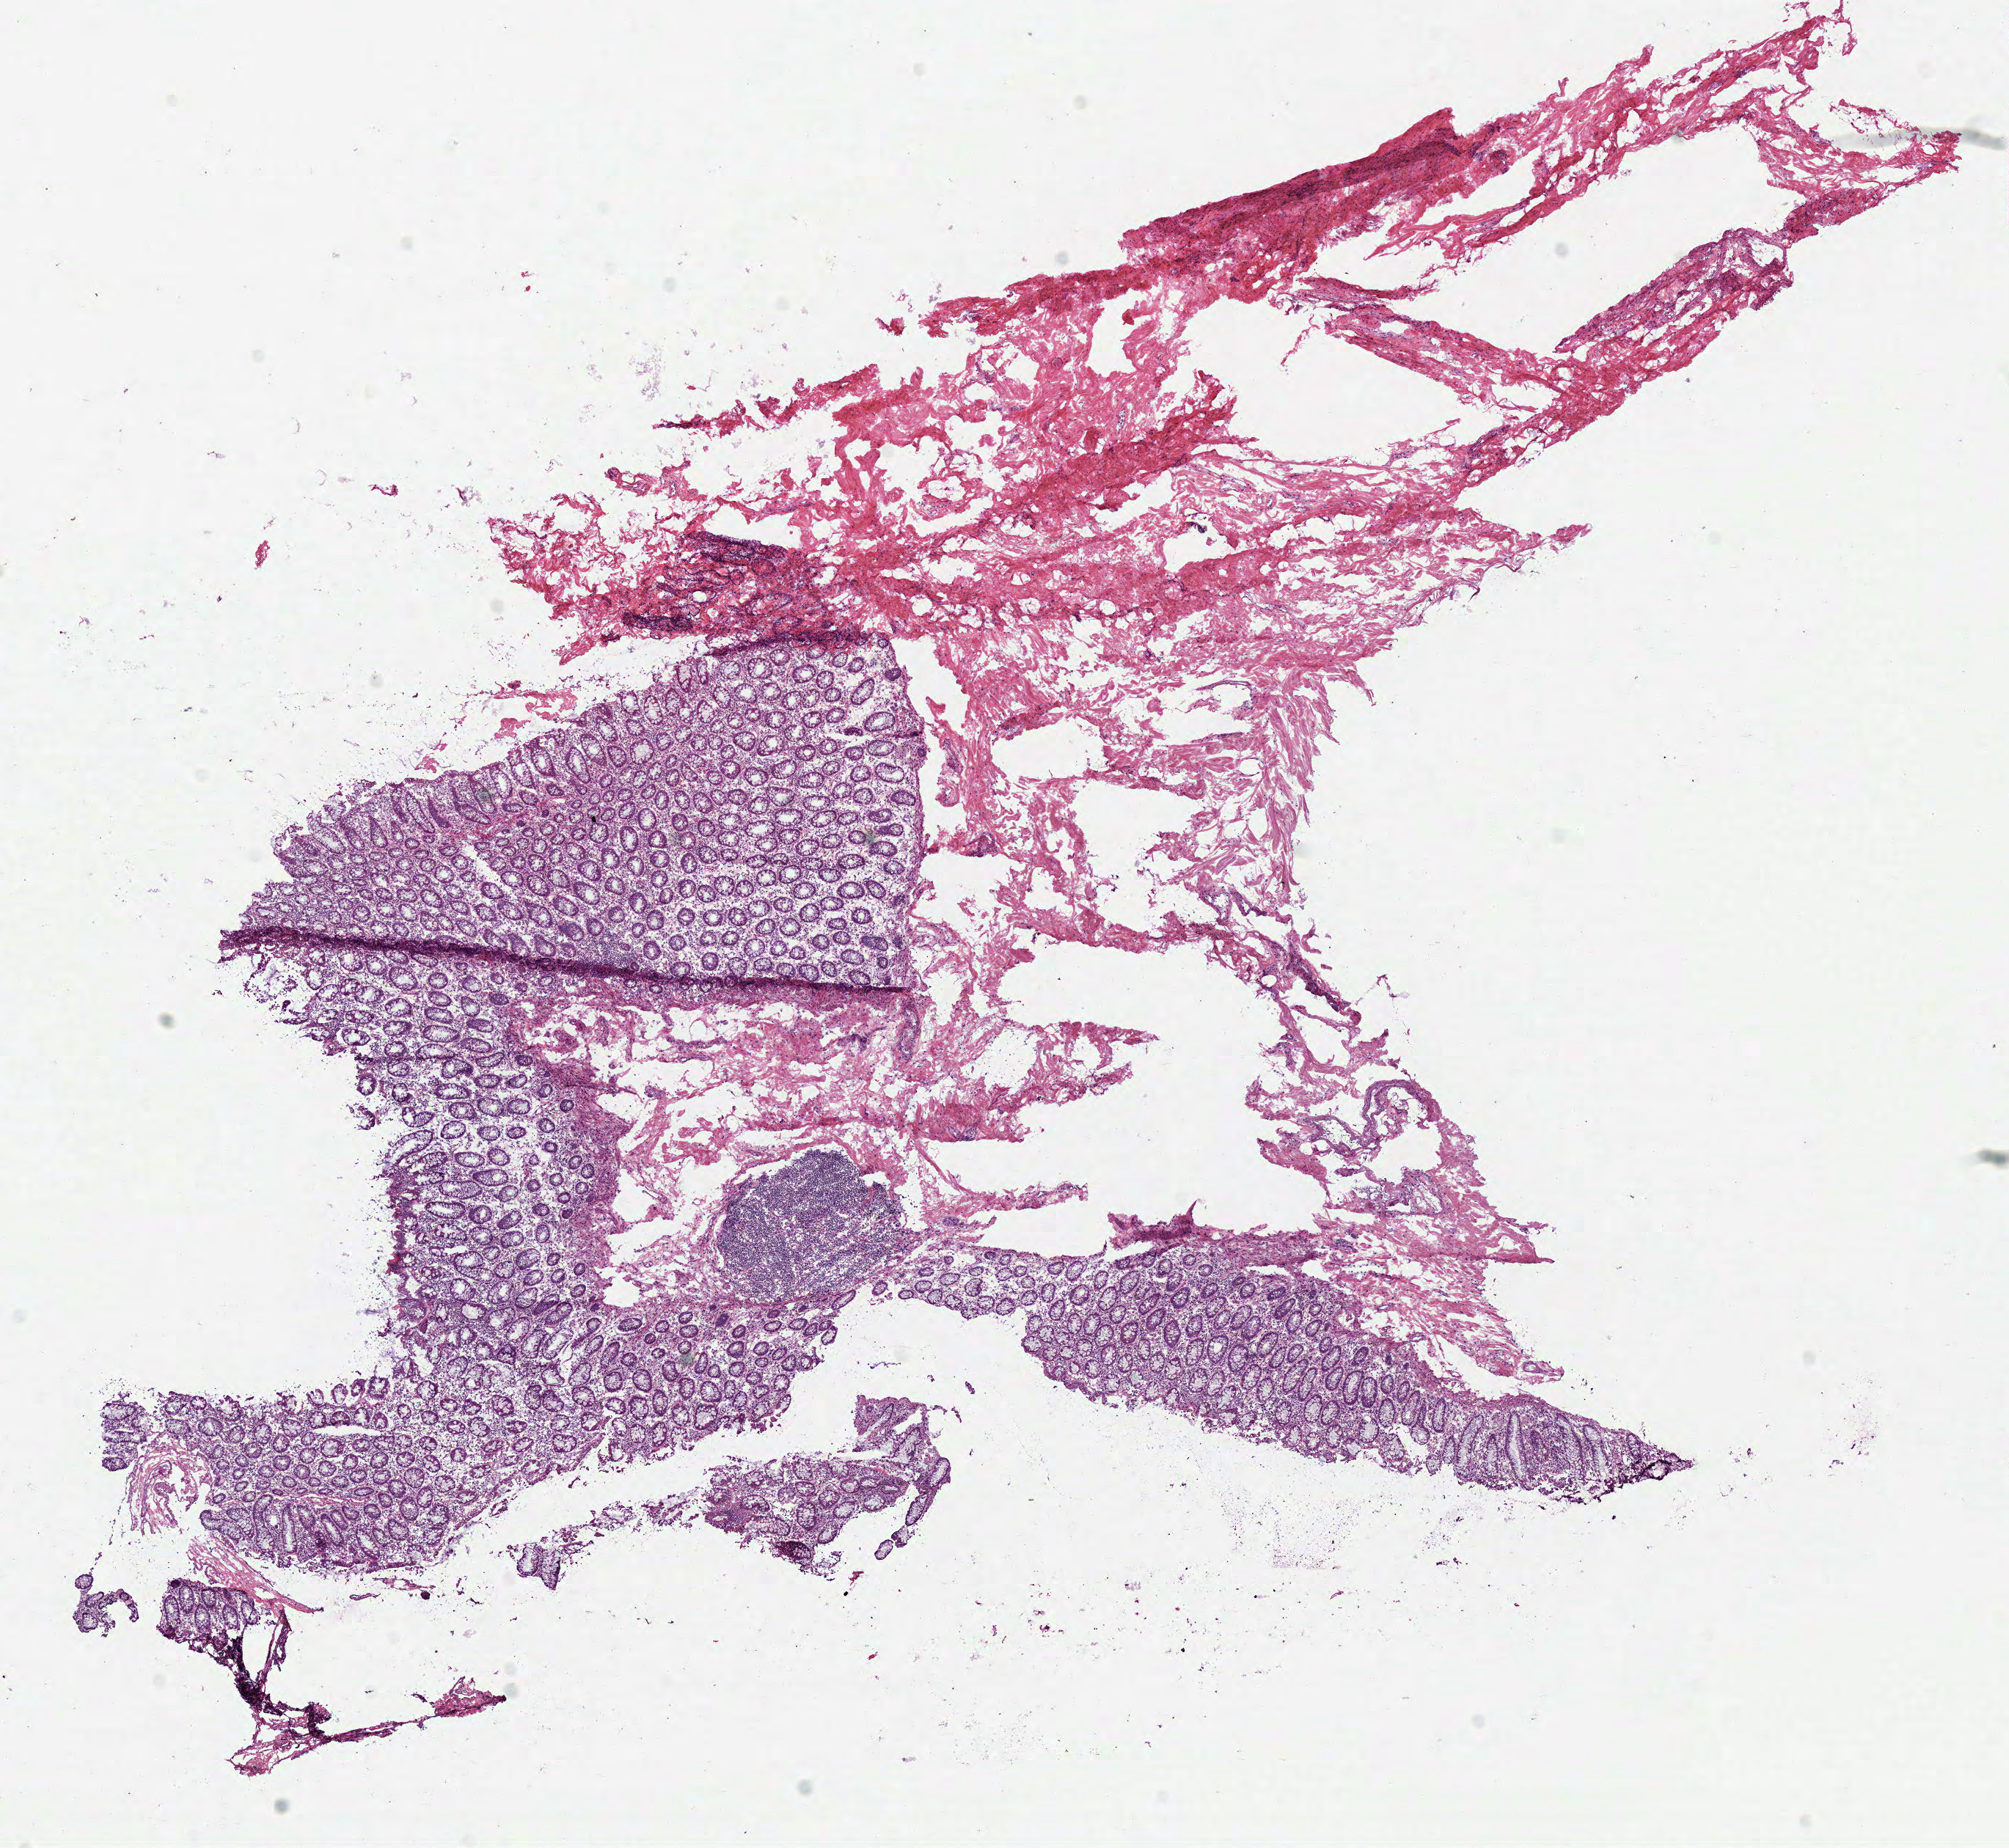
Whole-slide histology image, H&E, a low-resolution overview of the entire scanned area, about 10.8 x 9.9 mm (acquisition: 40x scan). Frozen section from the top of the tissue portion. Solid tissue normal (non-tumour tissue) sample from the colon. Patient: male, age at initial diagnosis 81 years.
This section: solid tissue normal sample (biorepository sample class). Patient diagnosis: Adenocarcinoma, NOS (cecum).